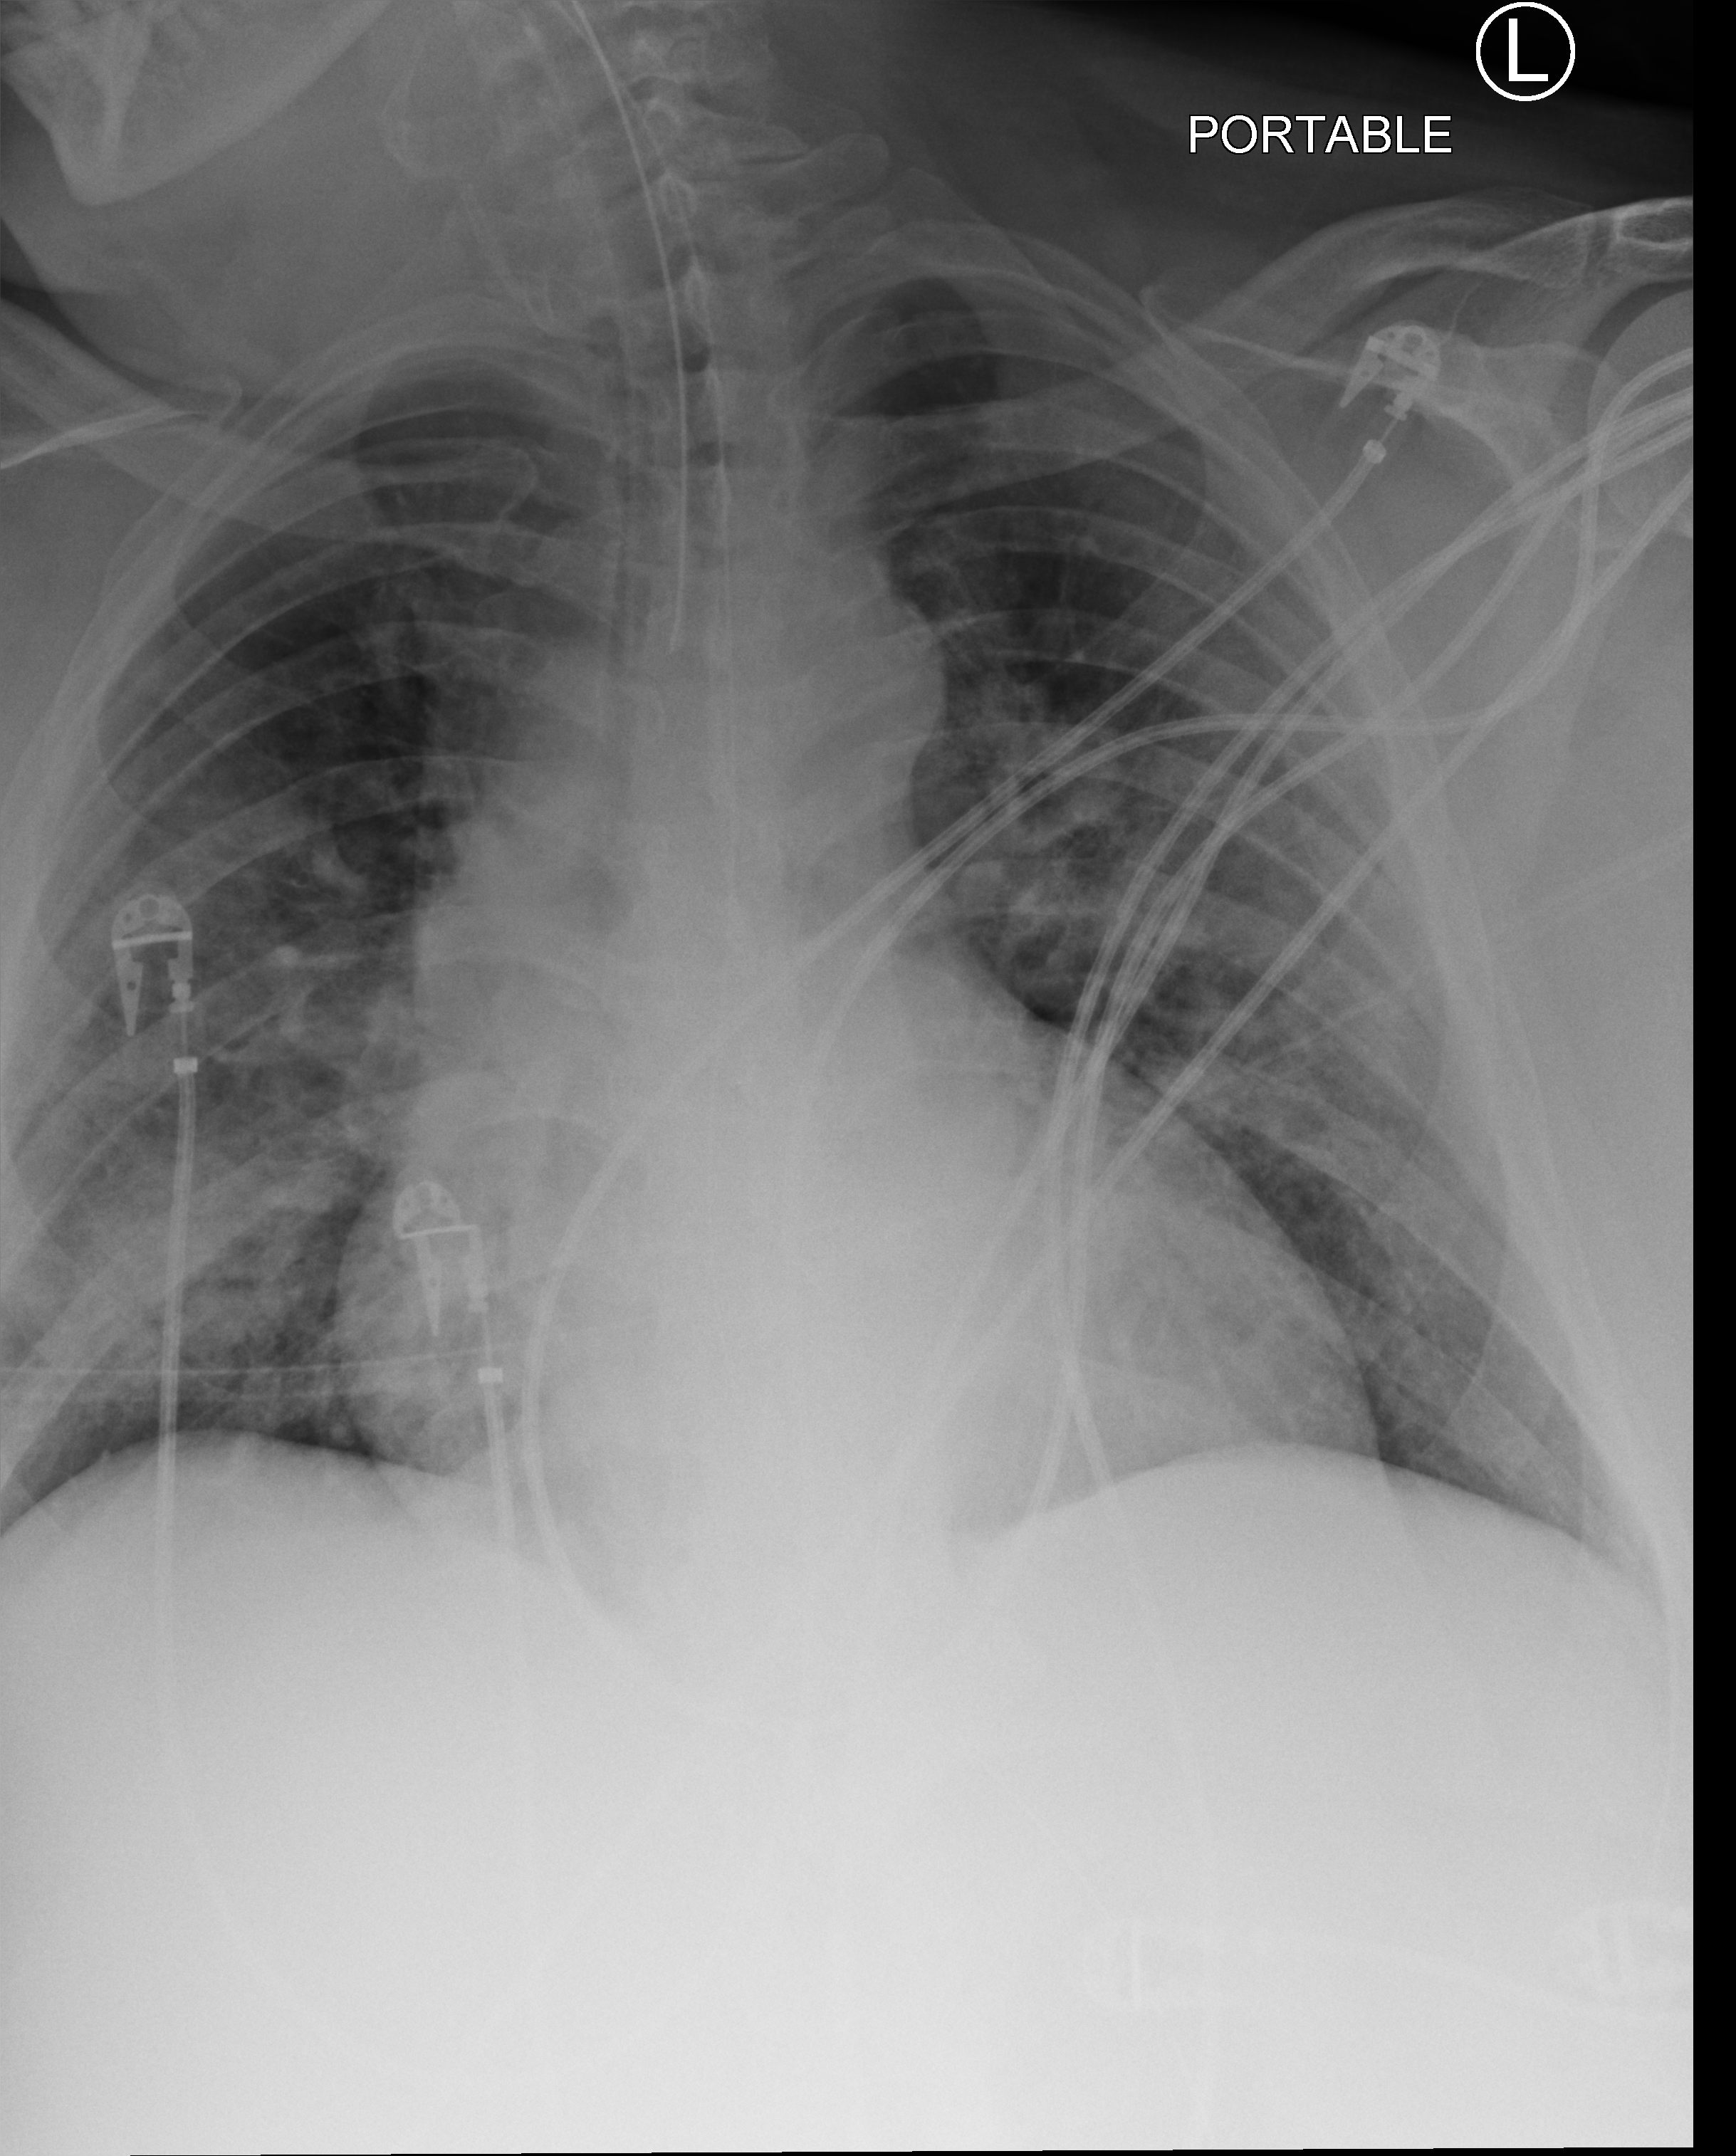
Bedside chest radiograph (computed radiography). Patient hospitalised with COVID-19; male, aged 60–74 years.
Admission-level facts for this patient (not findings on this image; timing relative to this image not recorded):
- smoking status (admission record): former